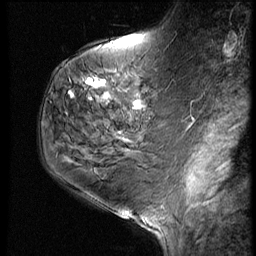
Breast MRI (dynamic contrast-enhanced), one sagittal slice; position 24 of 60 along the scan axis; 3 images stored at this slice position (order not interpretable as contrast timing); 1.5 T; TE 4.2 ms, TR 9 ms; 2.5 mm slice thickness; 256 × 256 image matrix, field of view 180 × 180 mm. Female patient, age 59 years. Case-level facts recorded for this patient, not image findings: setting: breast cancer imaged before/during neoadjuvant chemotherapy; receptor status: HER2-positive.
Structures marked on this image (semi-automatically segmented with operator editing):
- analysis volume of interest (the breast-tissue region the enhancement analysis was run in; not a lesion): bounding box [x1, y1, x2, y2] px = [78, 61, 161, 125]
- tumour enhancement mask (voxels above the 140 % enhancement threshold inside the analysis volume of interest): [87, 79, 140, 106]